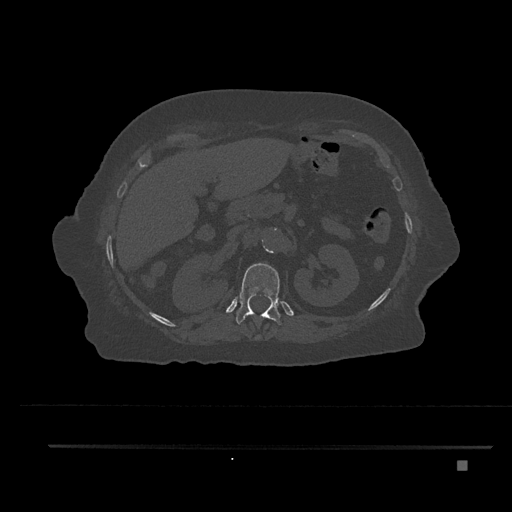
CT including the spine, one axial slice. Reconstruction kernel Br40s/3. 120 kVp. Bone window (W 1800 / L 400 HU). 0.5 mm slice thickness. 512 × 512 image matrix, field of view 437 × 437 mm. Patient: female, 76 years. From the clinical record (not read from this slice): primary cancer: lung; vertebrae with lytic lesions (as recorded): T11, L3.
Outlined on this slice (semi-automatic segmentation, software-assisted and operator-edited):
- T12 vertebra: bounding box [x1, y1, x2, y2] px = [236, 263, 282, 337]